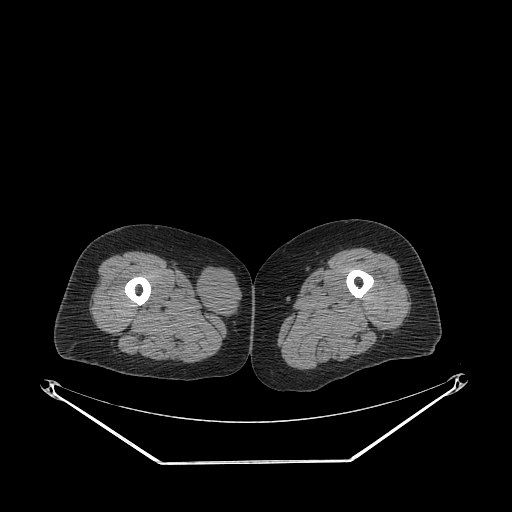
CT of an extremity soft-tissue mass (from a PET/CT study), one axial slice; position 235 of 311 along the scan axis; reconstruction kernel STANDARD; 140 kVp; soft-tissue window (W 400 / L 40 HU); 3.75 mm slice thickness; 512 × 512 image matrix, field of view 500 × 500 mm. Female patient. Case-level facts recorded for this patient, not image findings: histological type: leiomyosarcoma; grade: intermediate; site of the primary tumour: parascapusular.
Annotated regions visible in this slice (expert contour drawn on MRI and transferred to this co-registered scan by the dataset authors):
- gross tumour volume including surrounding oedema: bounding box [x1, y1, x2, y2] px = [196, 267, 241, 320]
- gross tumour volume (mass): [196, 267, 241, 320]